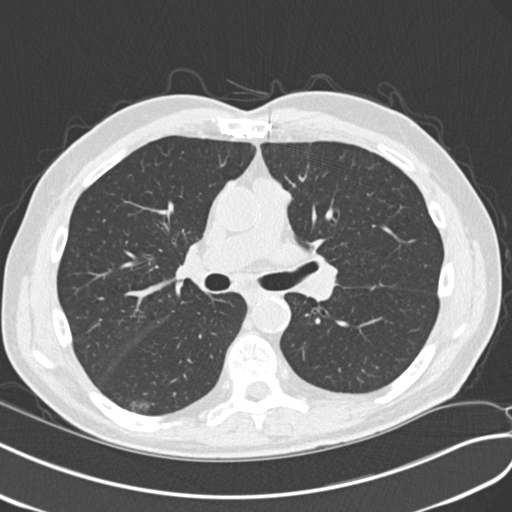
Chest CT (low-dose screening protocol), one axial image, second screening round (one year after baseline), lung window (W 1500 / L -600 HU), standard (soft-tissue) reconstruction kernel (B30f), 512 × 512 image matrix, field of view 354 × 354 mm. Male participant, aged 68 years at enrolment. Current smoker at enrolment.
Expert reader's lesion annotation, bounding box [x1, y1, x2, y2] px = [115, 387, 166, 424]. The screening reader recorded 4 non-calcified nodules or masses ≥4 mm on this exam (right upper lobe, left upper lobe, right upper lobe, right lower lobe); which of them this box marks is not recorded.